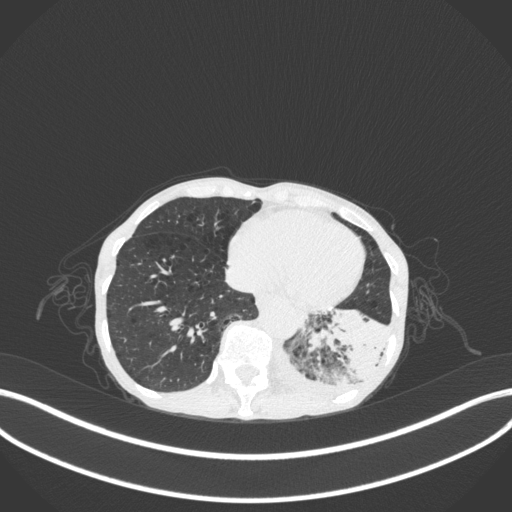
Chest CT, one axial slice. Slice 58 of 347 in the series (ordered by position). Reconstruction kernel B31f. Lung window (W 1500 / L -600 HU). 512 × 512 image matrix. Patient: female, 70 years. Case-level facts recorded for this patient, not image findings: clinical TNM (as recorded): T3 N0 M0; histopathological grade: G3.
Outlined on this slice (rectangle marked by the reading radiologist):
- lung tumour (recorded histology: small cell carcinoma): bounding box (x1, y1, x2, y2) in pixels: (303, 299, 393, 387)